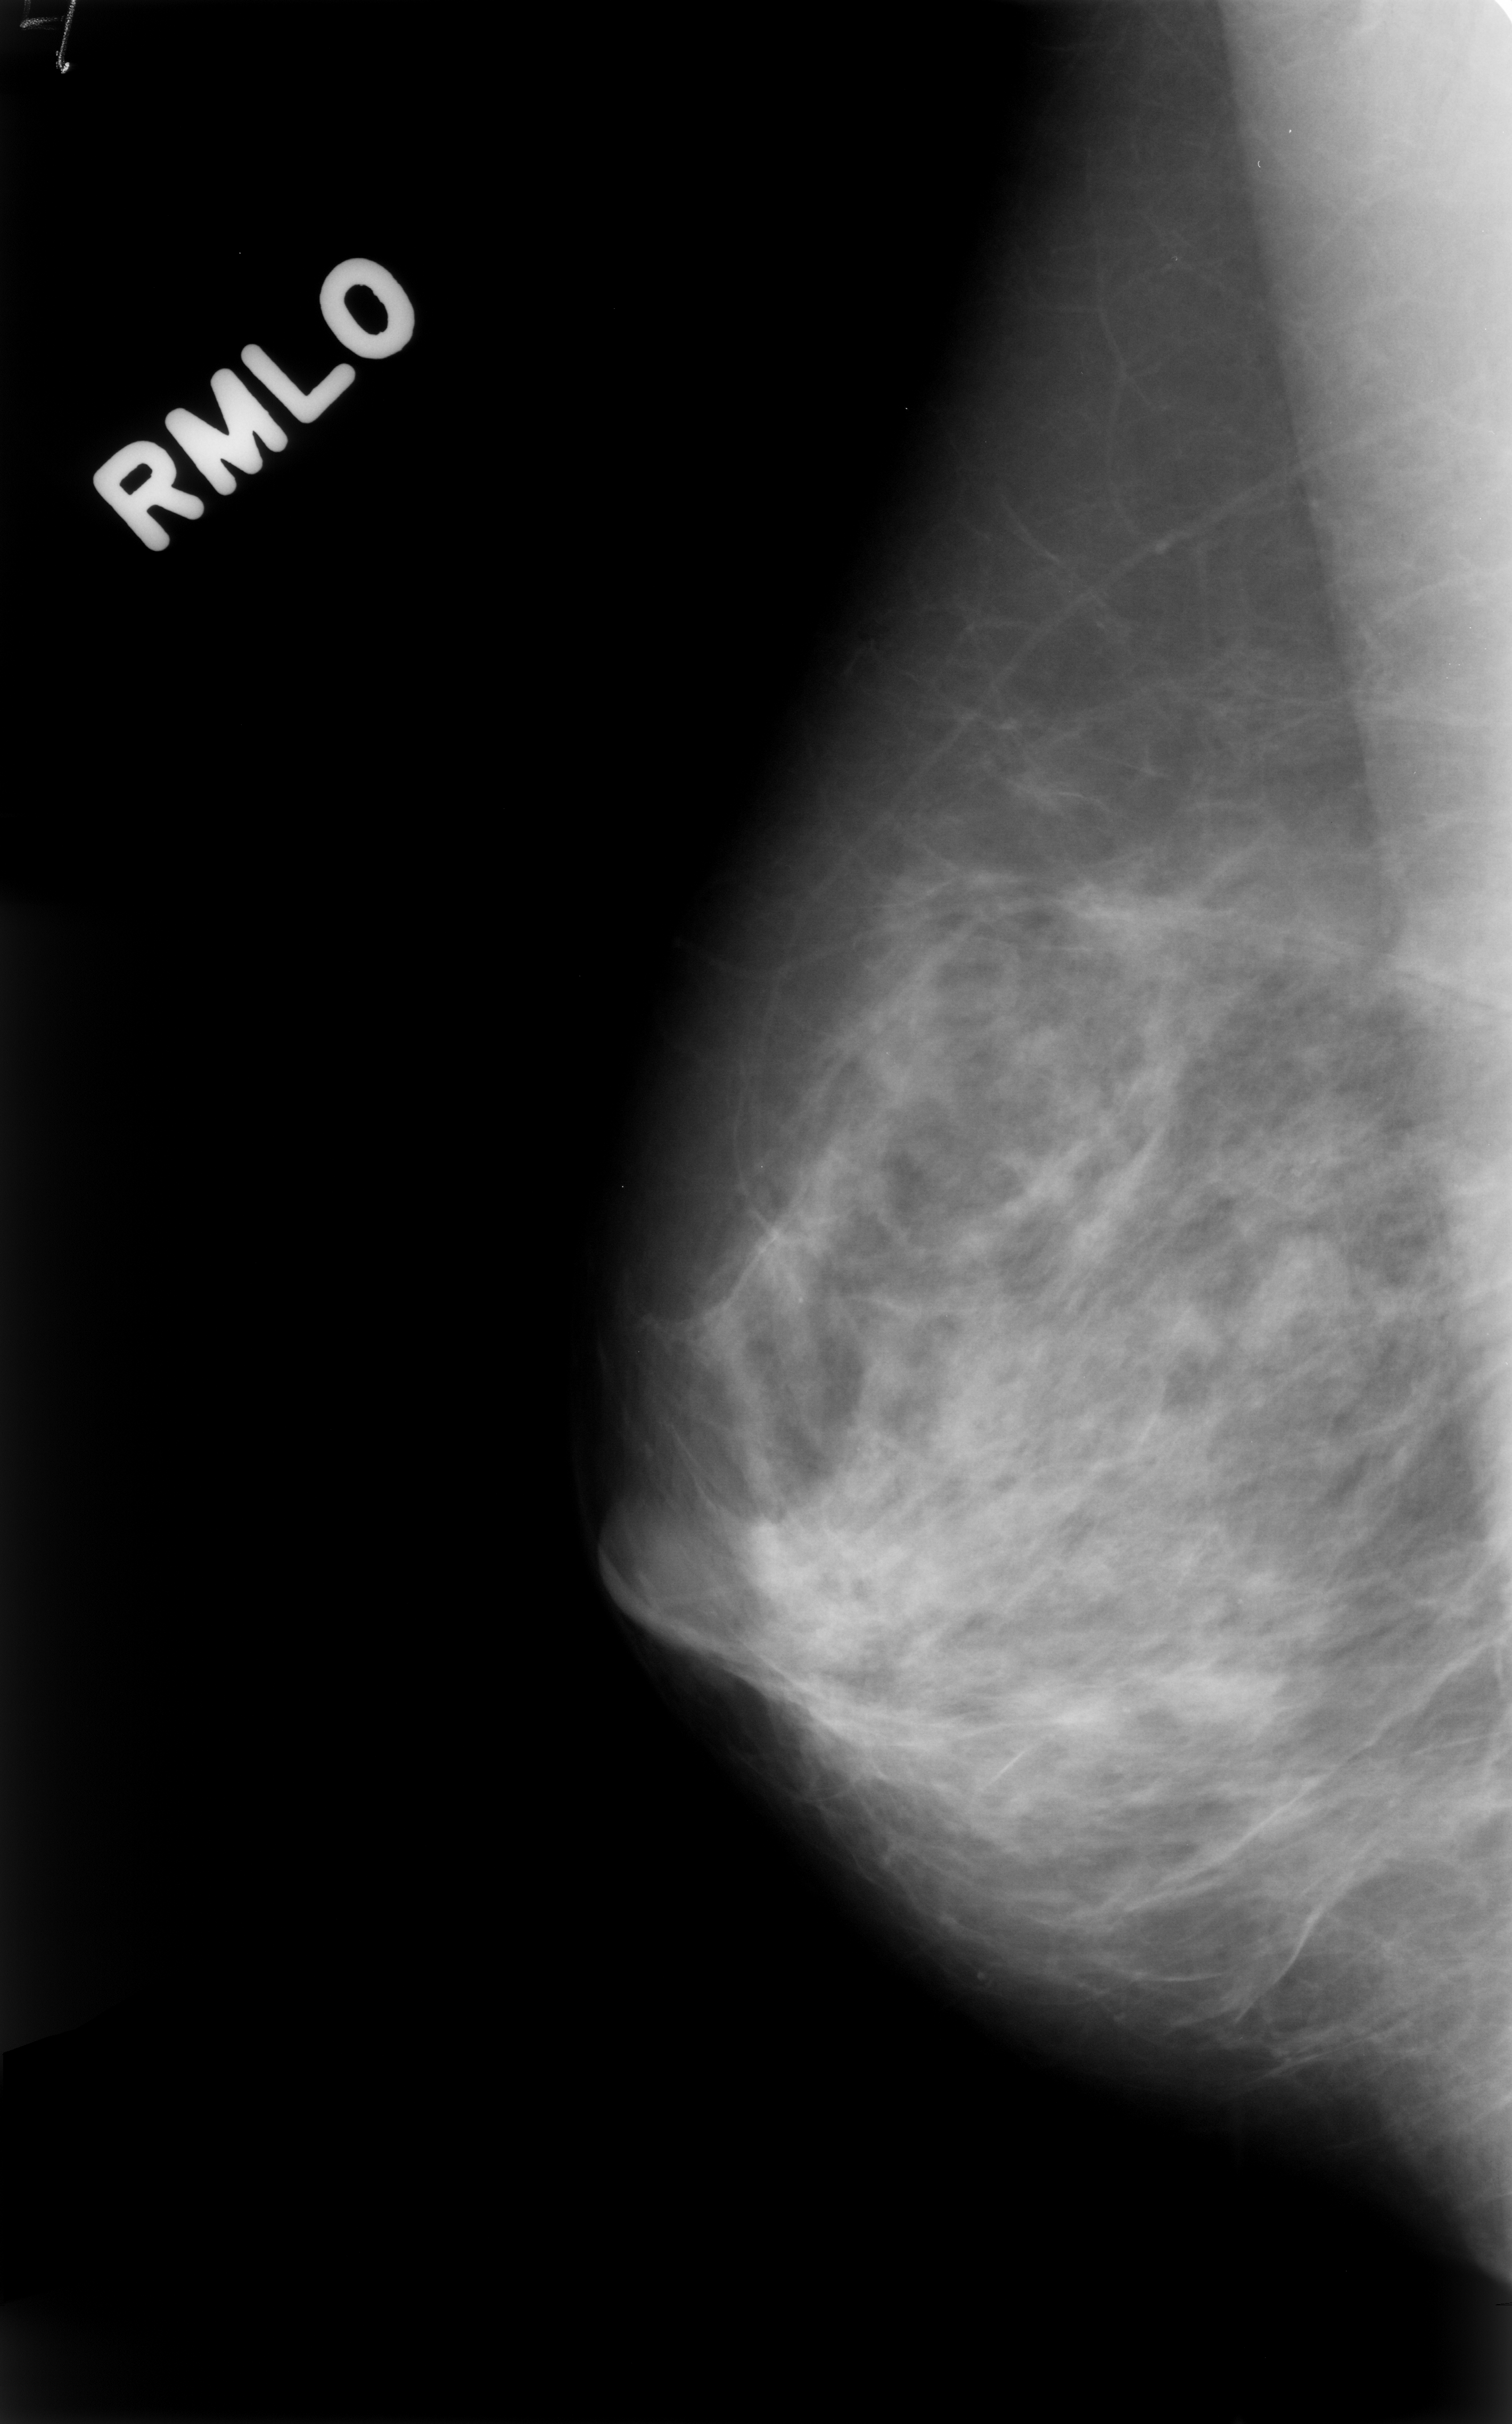
Scanned film-screen mammogram; right breast; mediolateral oblique (MLO) view; BI-RADS breast density category 2 (scale 1–4).
- Mass, shape lobulated, margins circumscribed; BI-RADS assessment category 4; pathology (as recorded): benign.